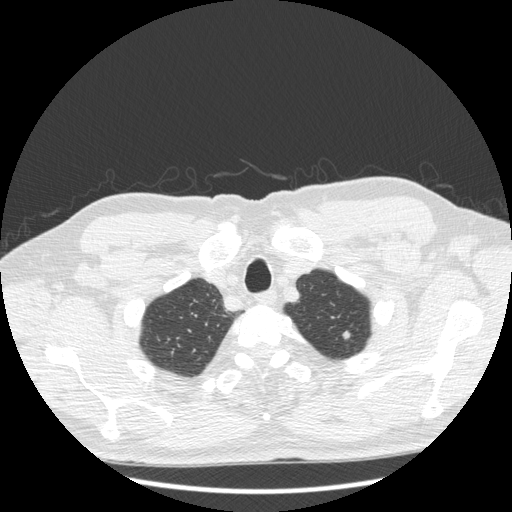
Low-dose screening chest CT, one axial slice; slice 195 of 223 in the series (ordered by position); reconstruction kernel STANDARD; lung window (W 1500 / L -600 HU); 1.25 mm slice thickness; 512 × 512 image matrix.
Annotated regions visible in this slice (manually delineated by an expert):
- lesion 1 (tumor, upper lobe of left lung): bounding box <343,331,350,339> (left, top, right, bottom; pixels)